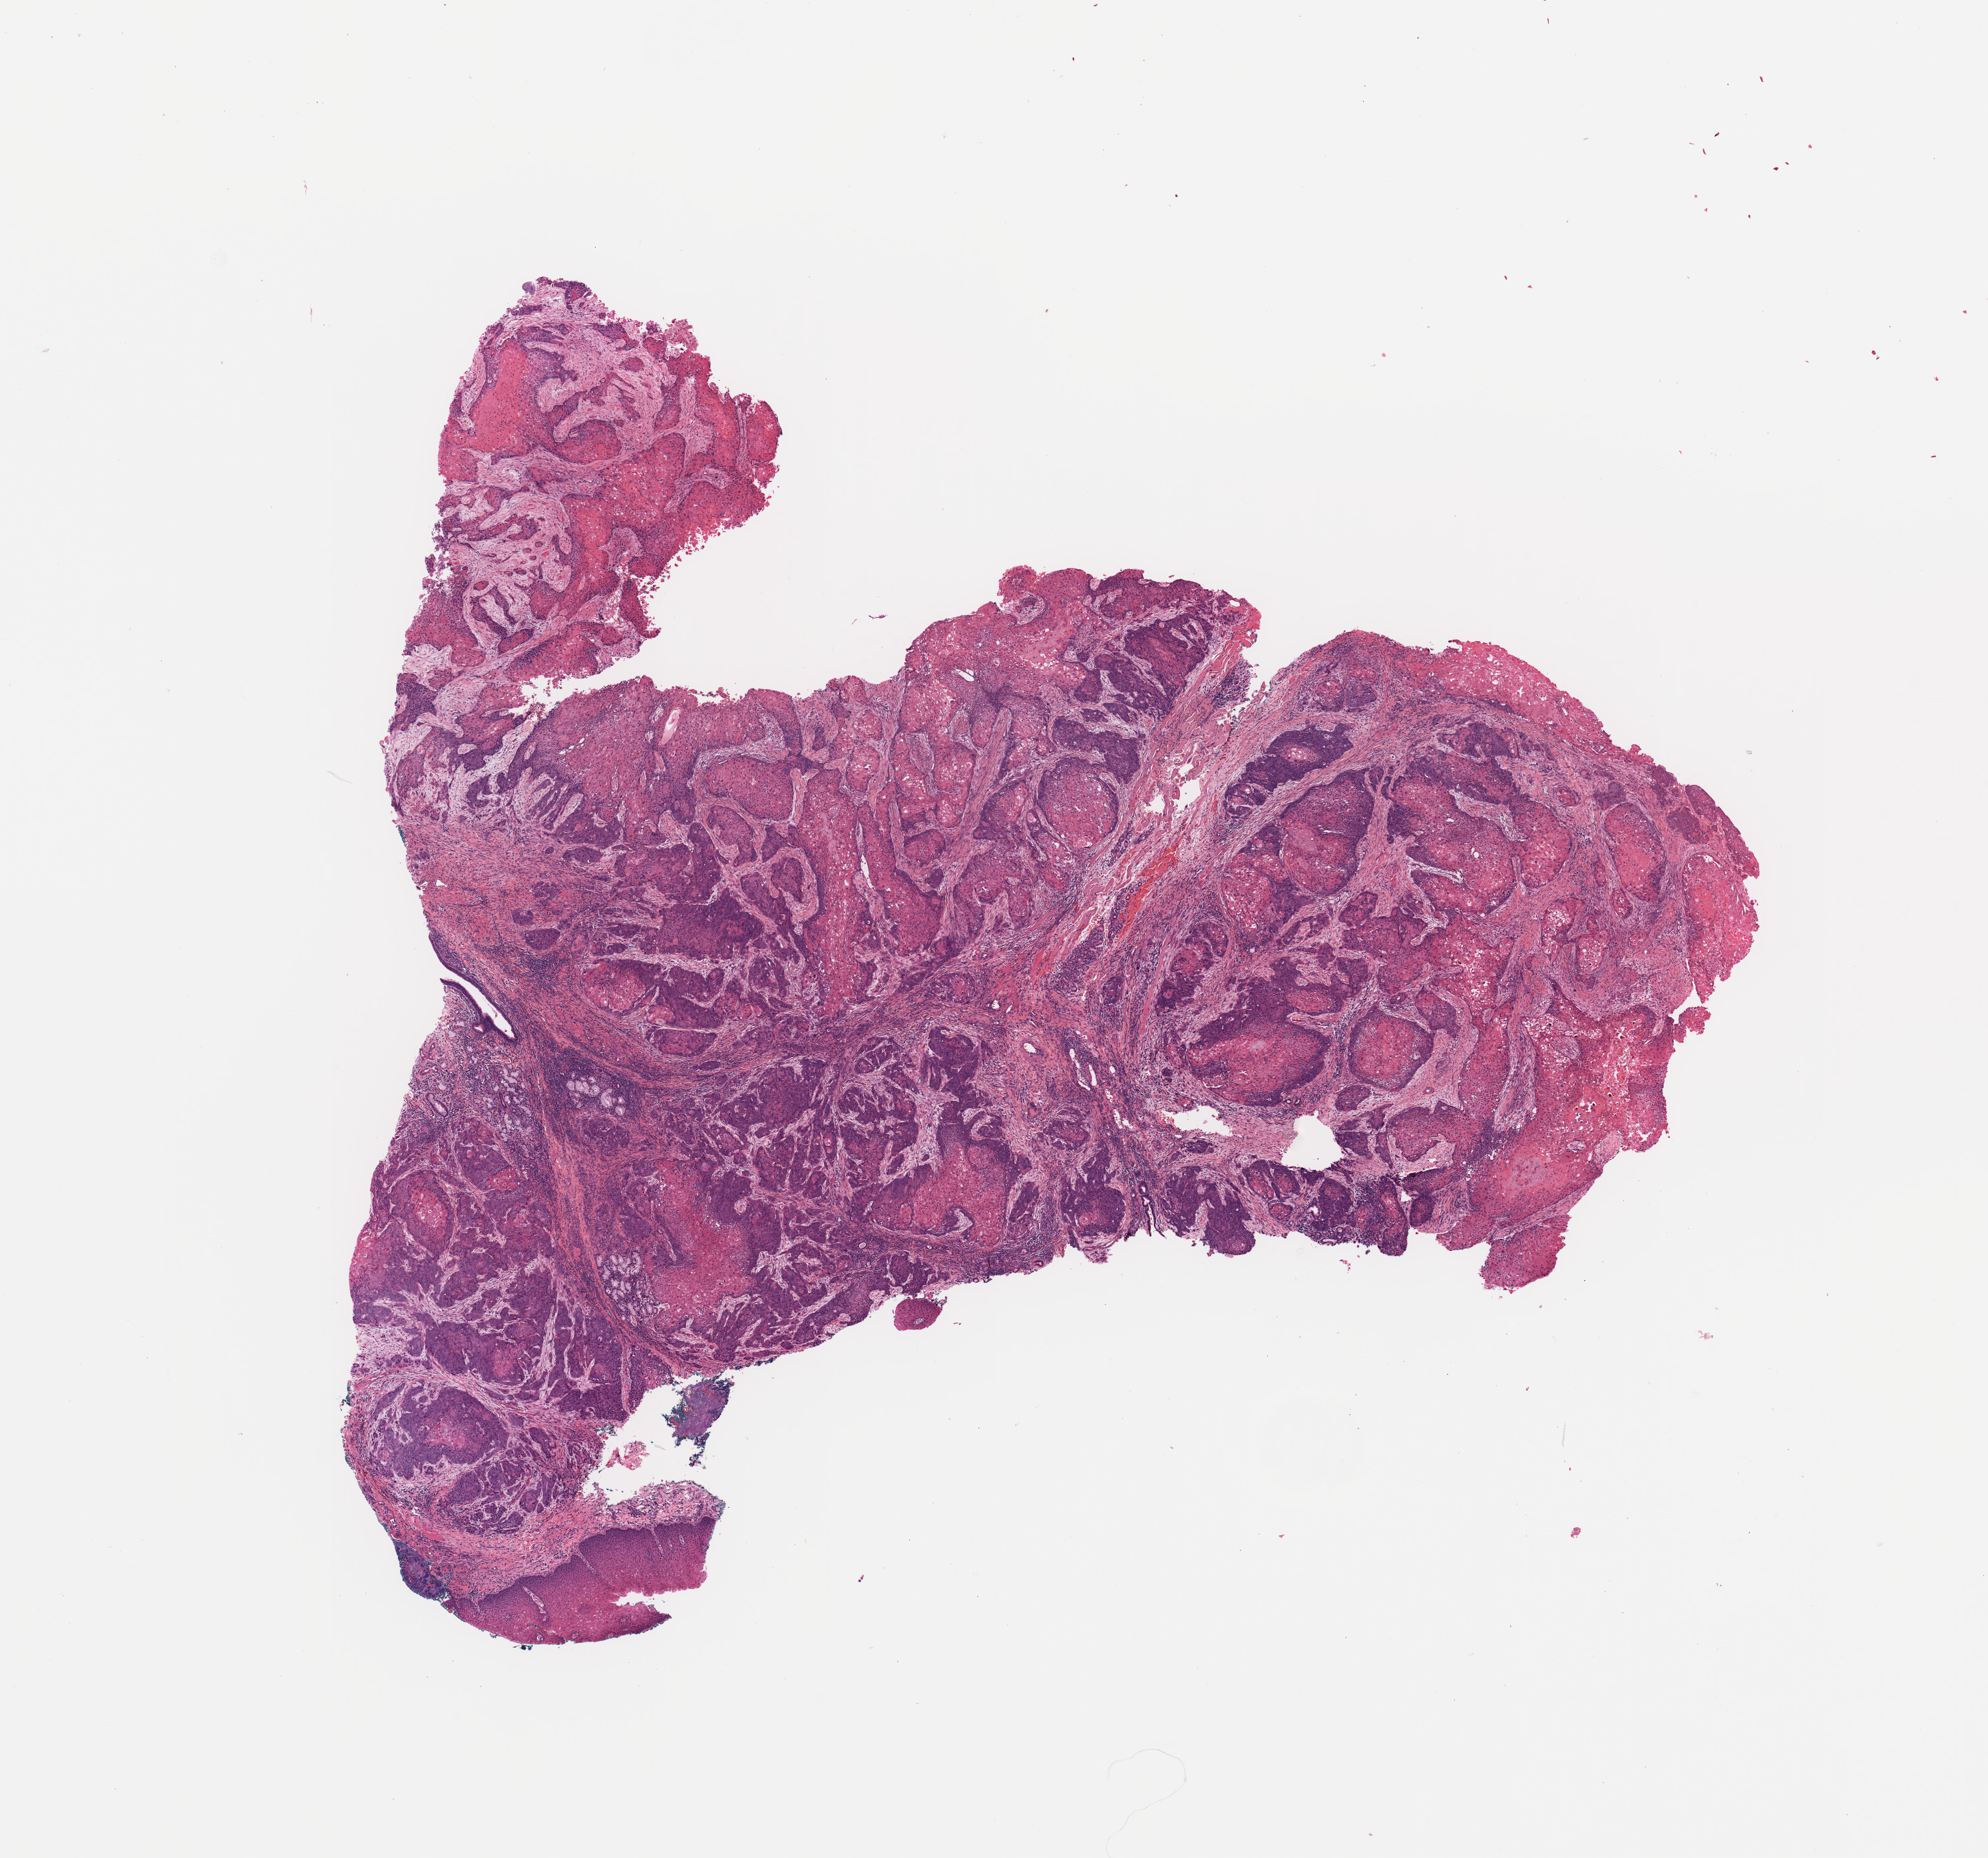
Hematoxylin and eosin (H&E) stained whole-slide image — shown as a low-resolution overview of the whole scanned area (about 11.8 x 11.0 mm, slide scanned at 20x); head and neck, tissue type not recorded. Male, 61 y/o.
Patient diagnosis: Squamous cell carcinoma, NOS (tongue, NOS).